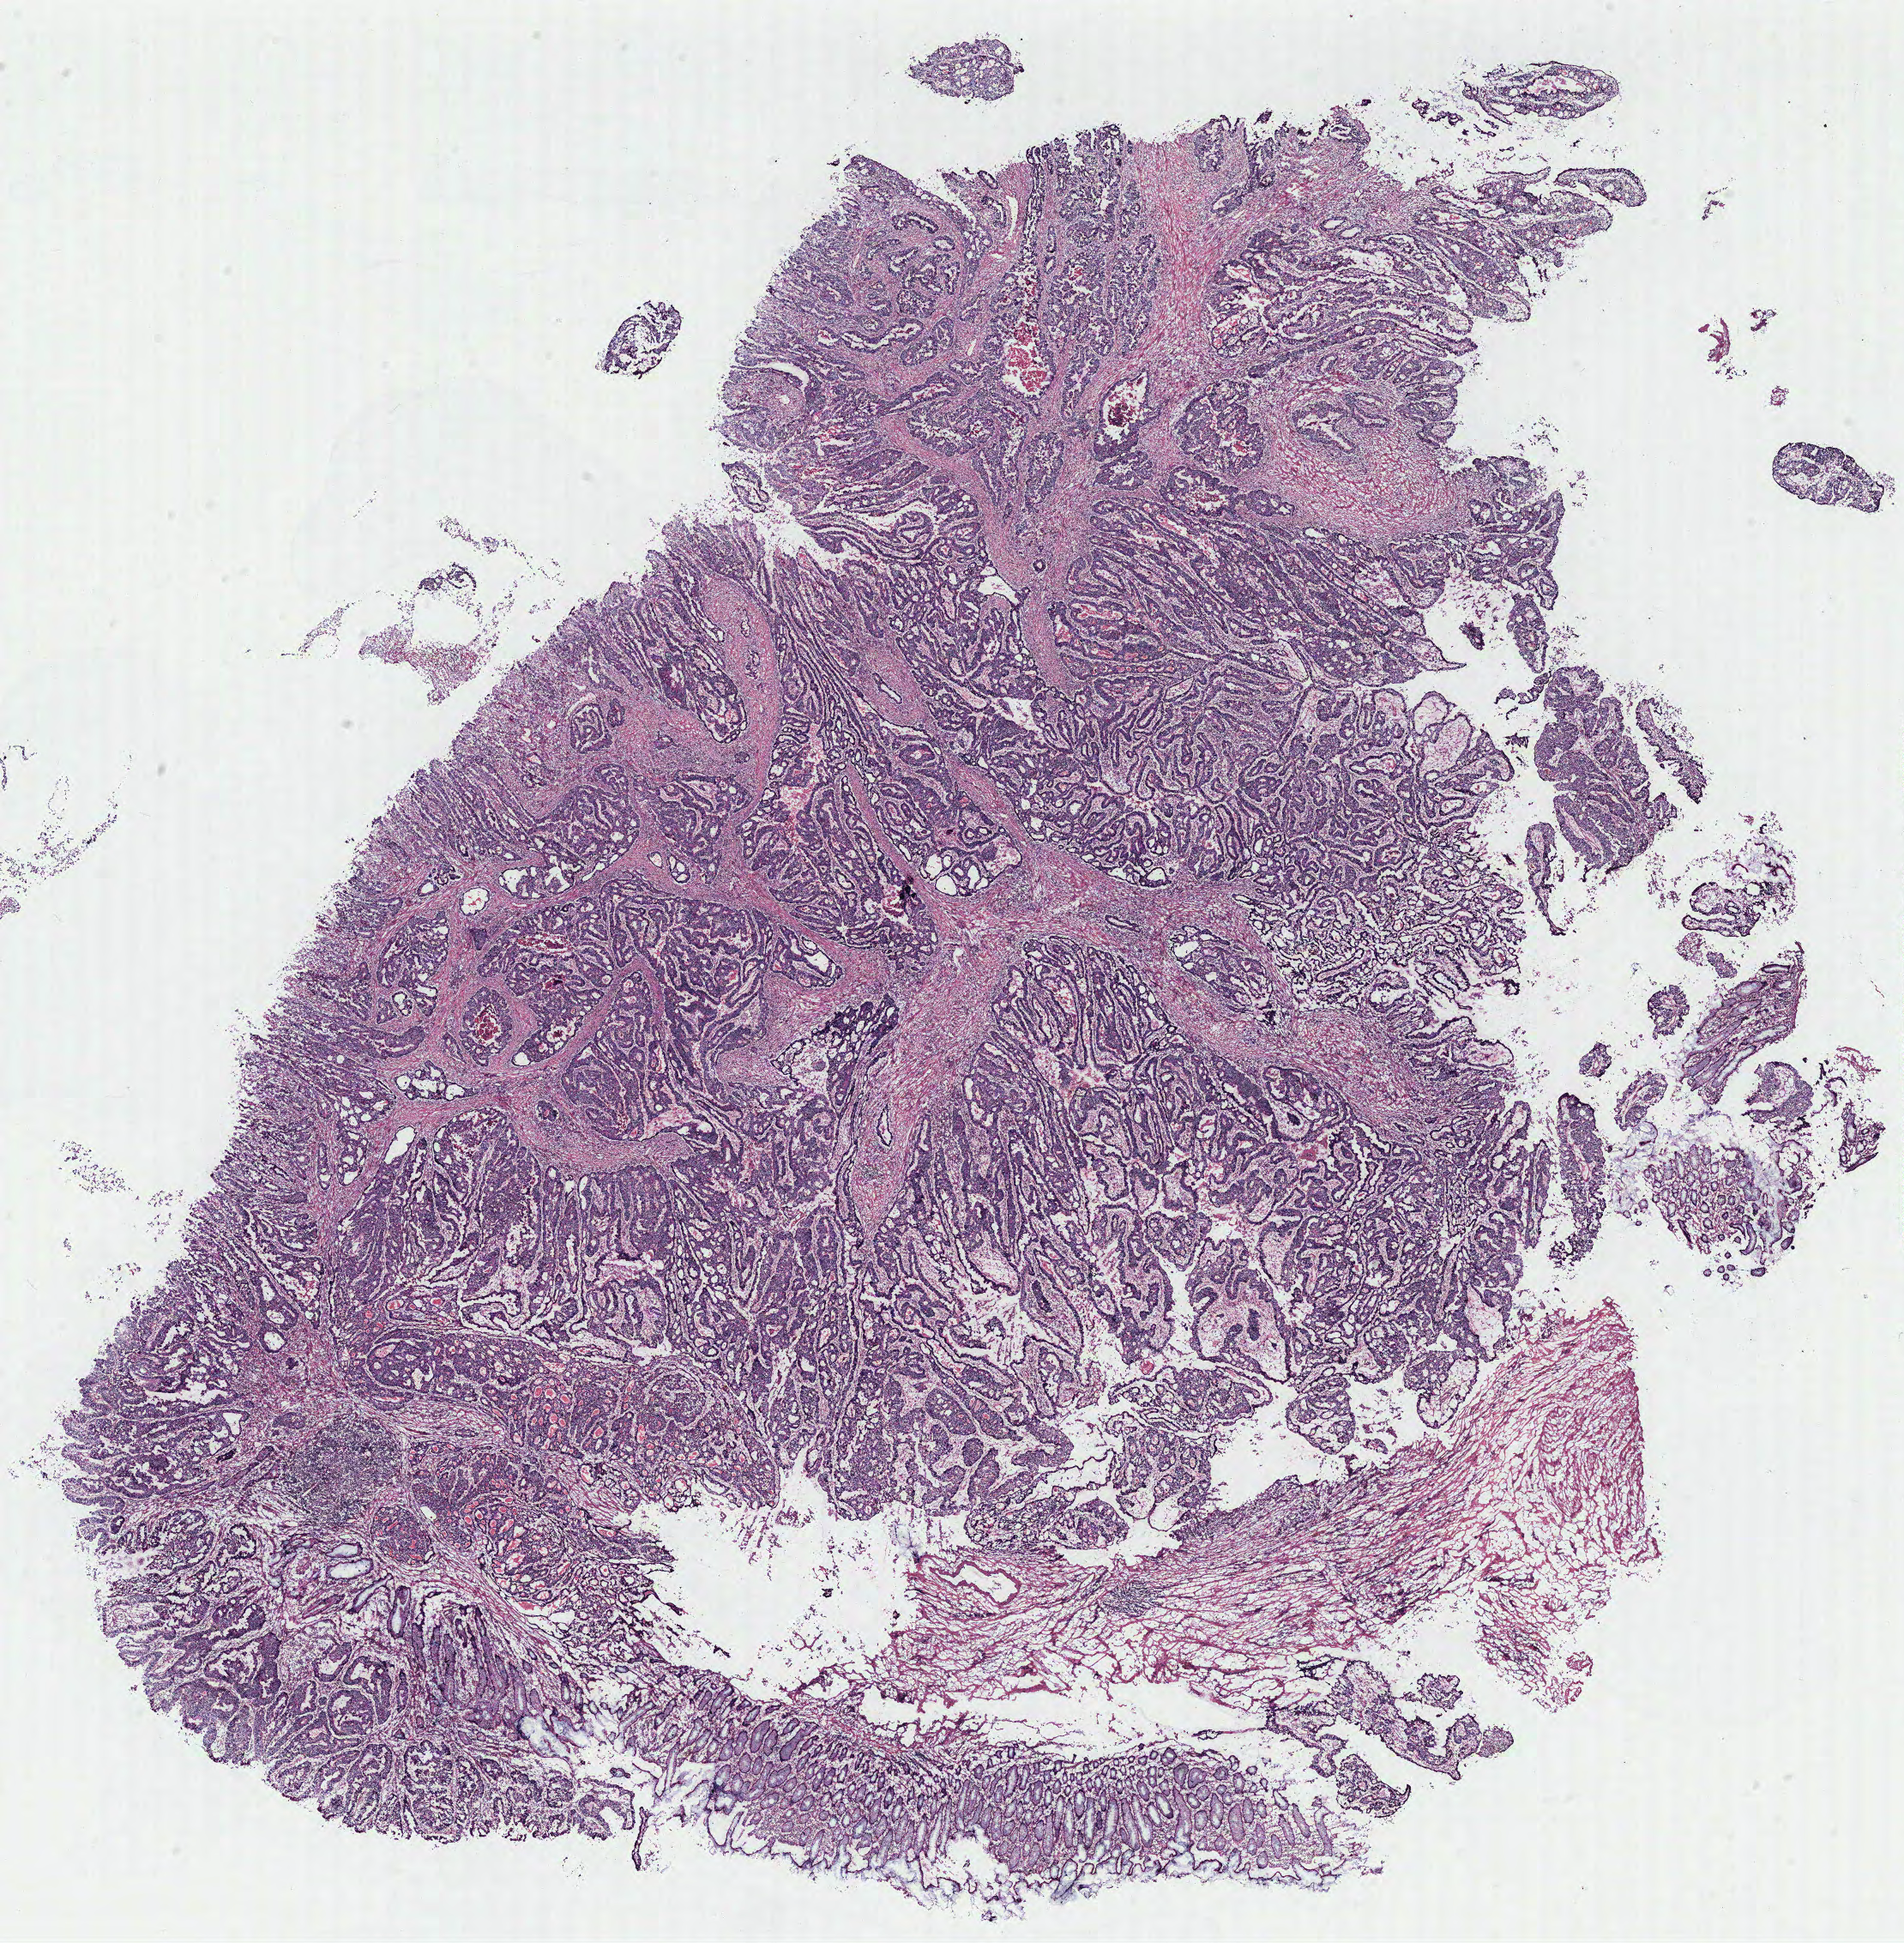
Whole-slide histology image, H&E-stained — a low-resolution overview of the entire scanned area, about 17.8 x 18.1 mm (acquisition: 40x scan). Colon, normal (non-tumour) tissue. Female, 59 y/o.
- this section: normal (non-tumour) tissue from the same patient
- patient diagnosis: Adenocarcinoma, NOS